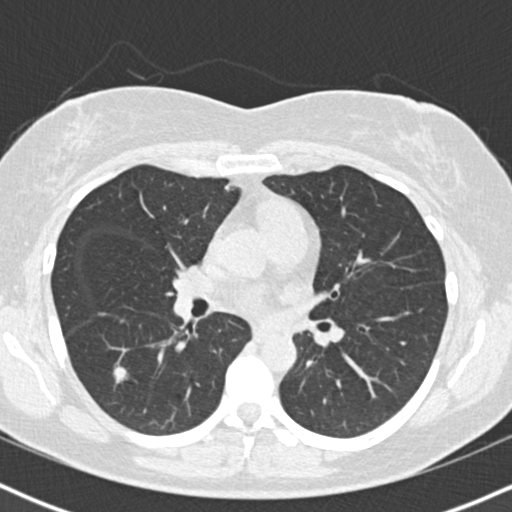
Low-dose screening chest CT, one axial slice. Position 93 of 167 along the scan axis. Reconstruction kernel B30f. 120 kVp. Lung window (W 1500 / L -600 HU). 512 × 512 image matrix, field of view 320 × 320 mm.
Annotated regions visible in this slice (expert manual segmentation):
- lesion 1 (tumor, lower lobe of right lung): bounding box <113,365,127,384> (left, top, right, bottom; pixels)